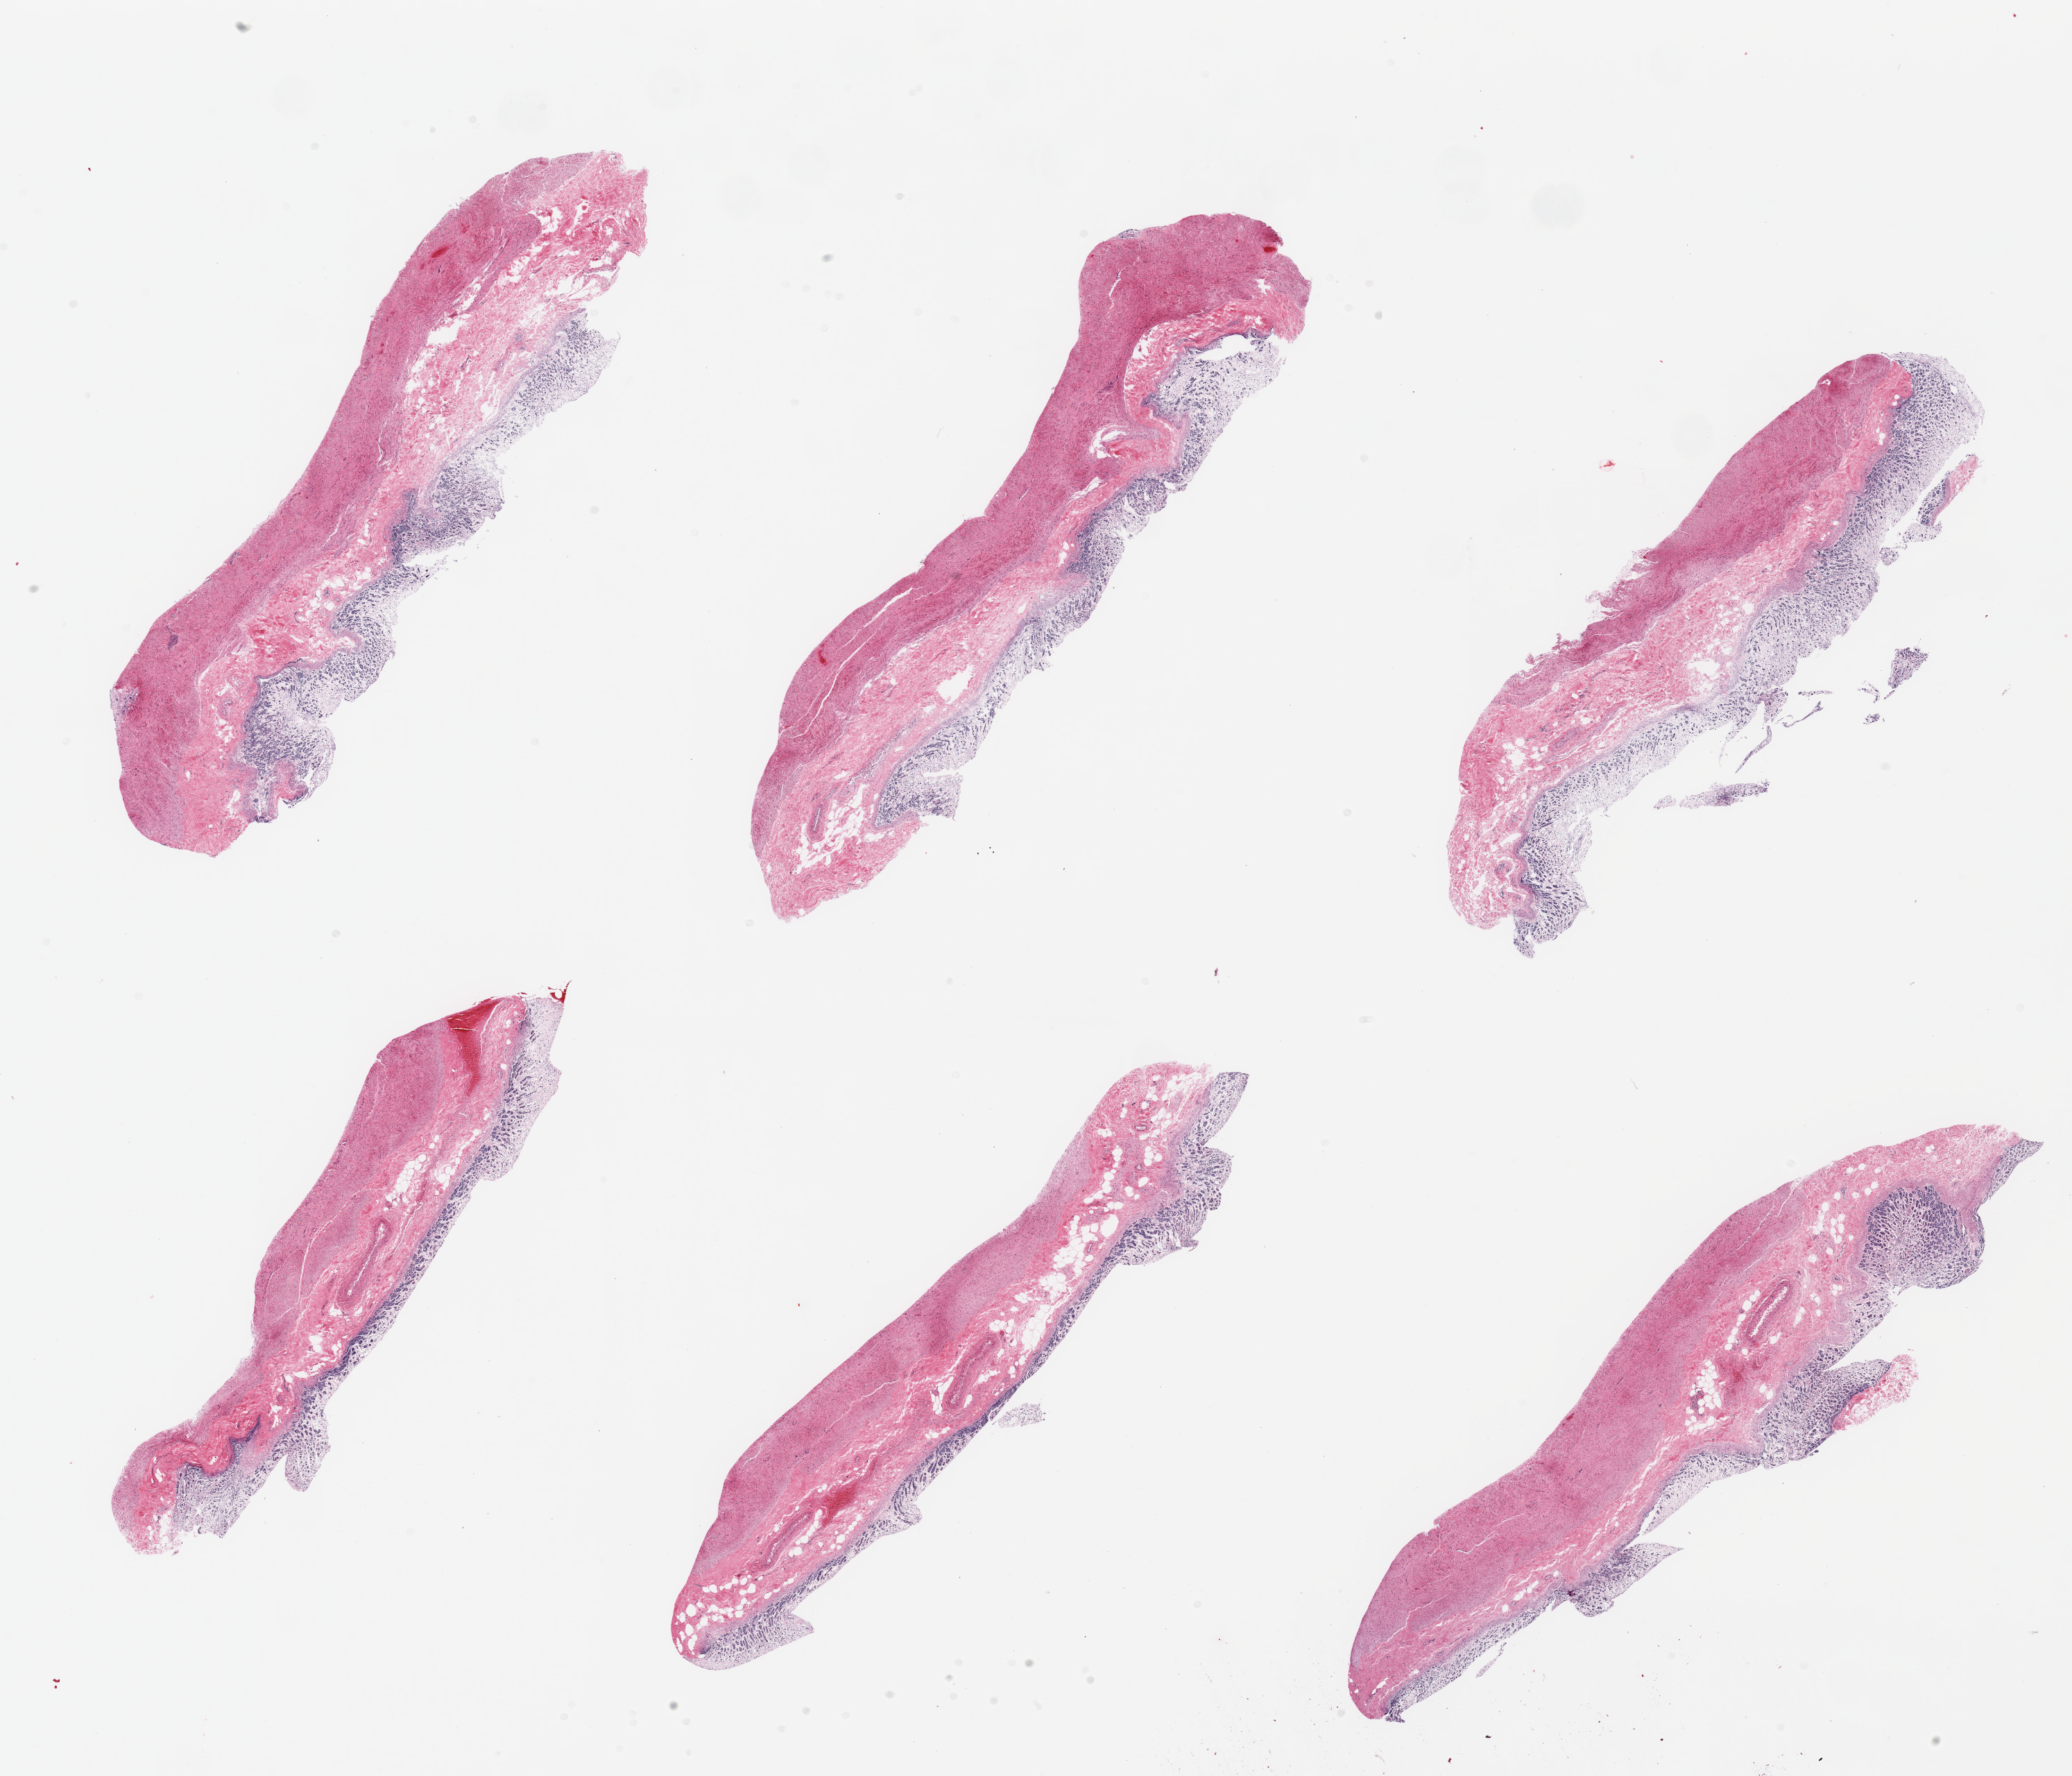
Digitized hematoxylin and eosin (H&E)-stained section, a low-resolution overview of the entire scanned area, about 23.6 x 20.2 mm, PAXgene-fixed, paraffin-embedded tissue, sampled site (target tissue): stomach, tissue donor sample. Male donor.
Review note (as recorded): 6 pieces, target mucosa up to ~0.8mm with advanced autolysis/sloughing.